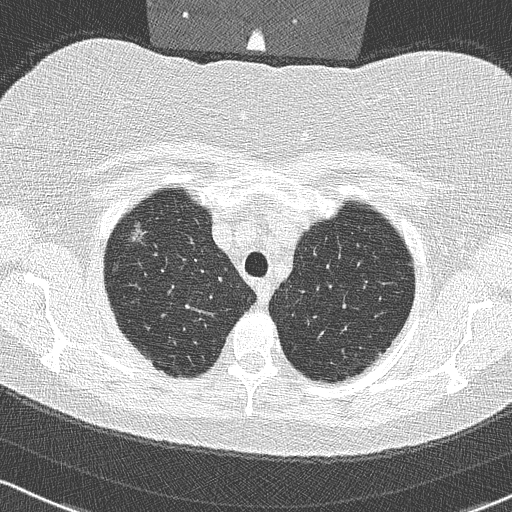
Low-dose screening chest CT, one axial slice; slice 267 of 315 in the series (ordered by position); reconstruction kernel B50f; lung window (W 1500 / L -600 HU); 2 mm slice thickness; 512 × 512 image matrix.
Structures marked on this image (outlined manually by an expert reader):
- lesion 1 (tumor, upper lobe of right lung): bounding box <131,221,148,243> (left, top, right, bottom; pixels)